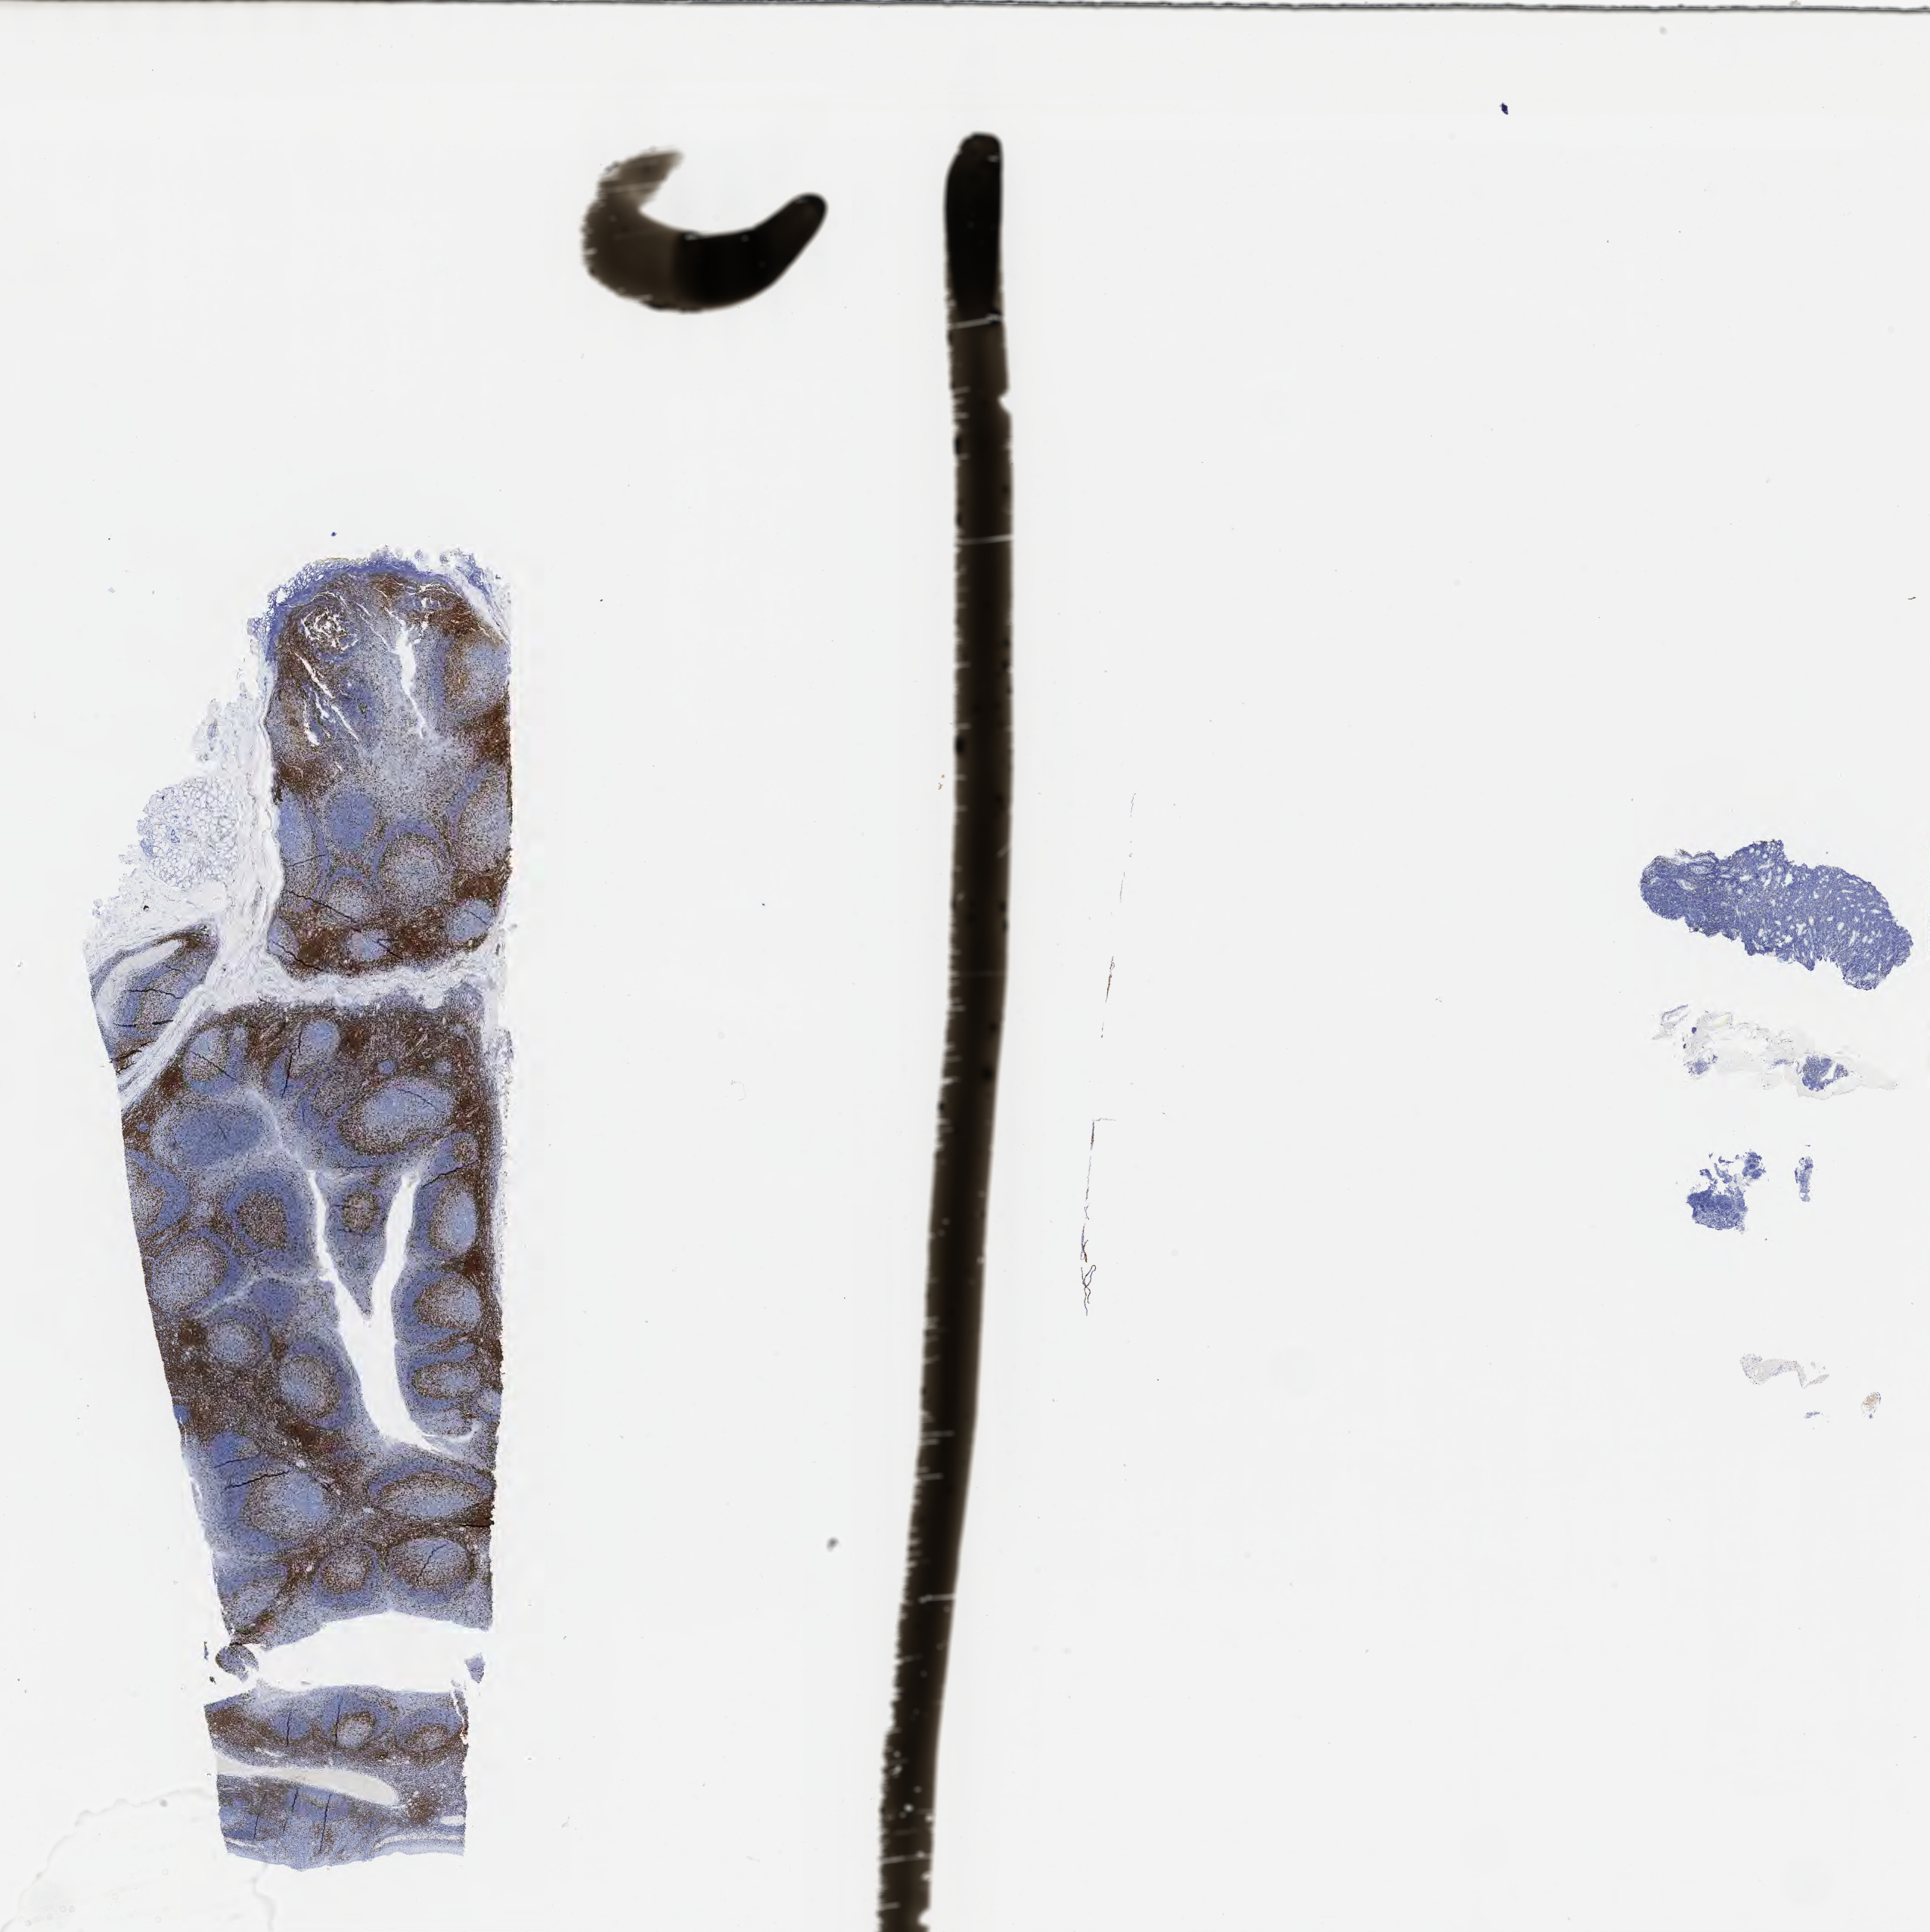
IHC for CD3, whole-slide image, shown as a low-resolution overview of the whole scanned area (about 20.6 x 20.7 mm); tumor tissue; site: stomach. Patient: female, 28 years old.
Histologic diagnosis: Burkitt lymphoma, NOS.